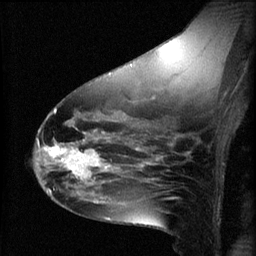
Breast MRI (dynamic contrast-enhanced), one sagittal slice. Position 35 of 60 along the scan axis. 3 images stored at this slice position (order not interpretable as contrast timing). 1.5 T. TE 4.2 ms, TR 8.2 ms. 2 mm slice thickness. 256 × 256 image matrix, field of view 180 × 180 mm. Female patient, age 49 years.
Outlined on this slice (semi-automatic segmentation, software-assisted and operator-edited):
- analysis volume of interest (the breast-tissue region the enhancement analysis was run in; not a lesion): bounding box (x1, y1, x2, y2) in pixels: (45, 136, 109, 187)
- tumour enhancement mask (voxels above the 70 % enhancement threshold inside the analysis volume of interest): (45, 140, 109, 185)